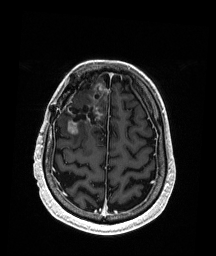
Brain MRI from a brain-tumour surgery series, one axial slice; slice 50 of 192 in the series (ordered by position); T1-weighted post-contrast; 216 × 256 image matrix. From the clinical record (not read from this slice): histopathology: Astrocytoma; WHO grade: 3; IDH mutation: yes.
Structures marked on this image (outlined manually by an expert reader):
- previous resection cavity: bounding box (x1, y1, x2, y2) in pixels: (64, 93, 101, 126)
- tumour: (68, 85, 109, 134)